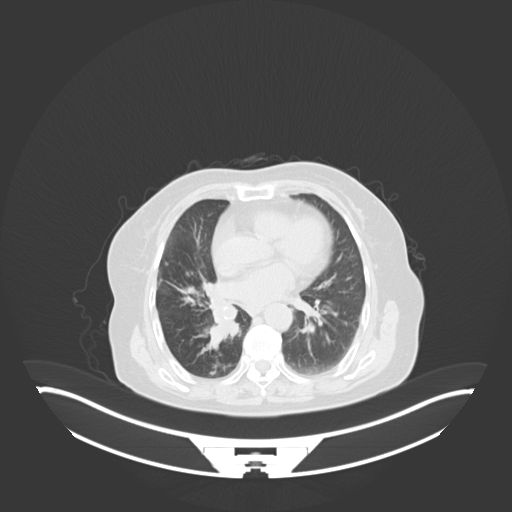
Chest CT, one axial slice; slice 24 of 76 in the series (ordered by position); lung window (W 1500 / L -600 HU); 3 mm slice thickness; 512 × 512 image matrix, field of view 500 × 500 mm. Female patient, age 75 years. From the clinical record (not read from this slice): clinical TNM (as recorded): T1b N0 M1a.
Outlined on this slice (bounding box drawn by a radiologist):
- lung tumour (recorded histology: squamous cell carcinoma): bounding box (x1, y1, x2, y2) in pixels: (202, 296, 242, 349)